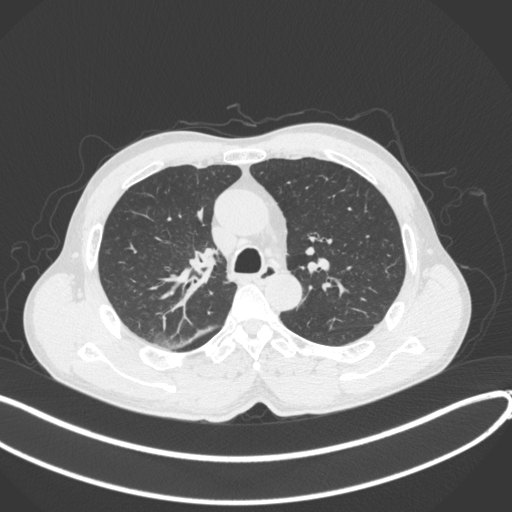
Chest CT, one axial slice. Position 266 of 409 along the scan axis. Lung window (W 1500 / L -600 HU). 1 mm slice thickness. 512 × 512 image matrix, field of view 400 × 400 mm. Male patient, age 53 years. From the clinical record (not read from this slice): clinical TNM (as recorded): T1b N0 M0.
Outlined on this slice (rectangle marked by the reading radiologist):
- lung tumour (recorded histology: squamous cell carcinoma): bounding box <186,247,223,282> (left, top, right, bottom; pixels)